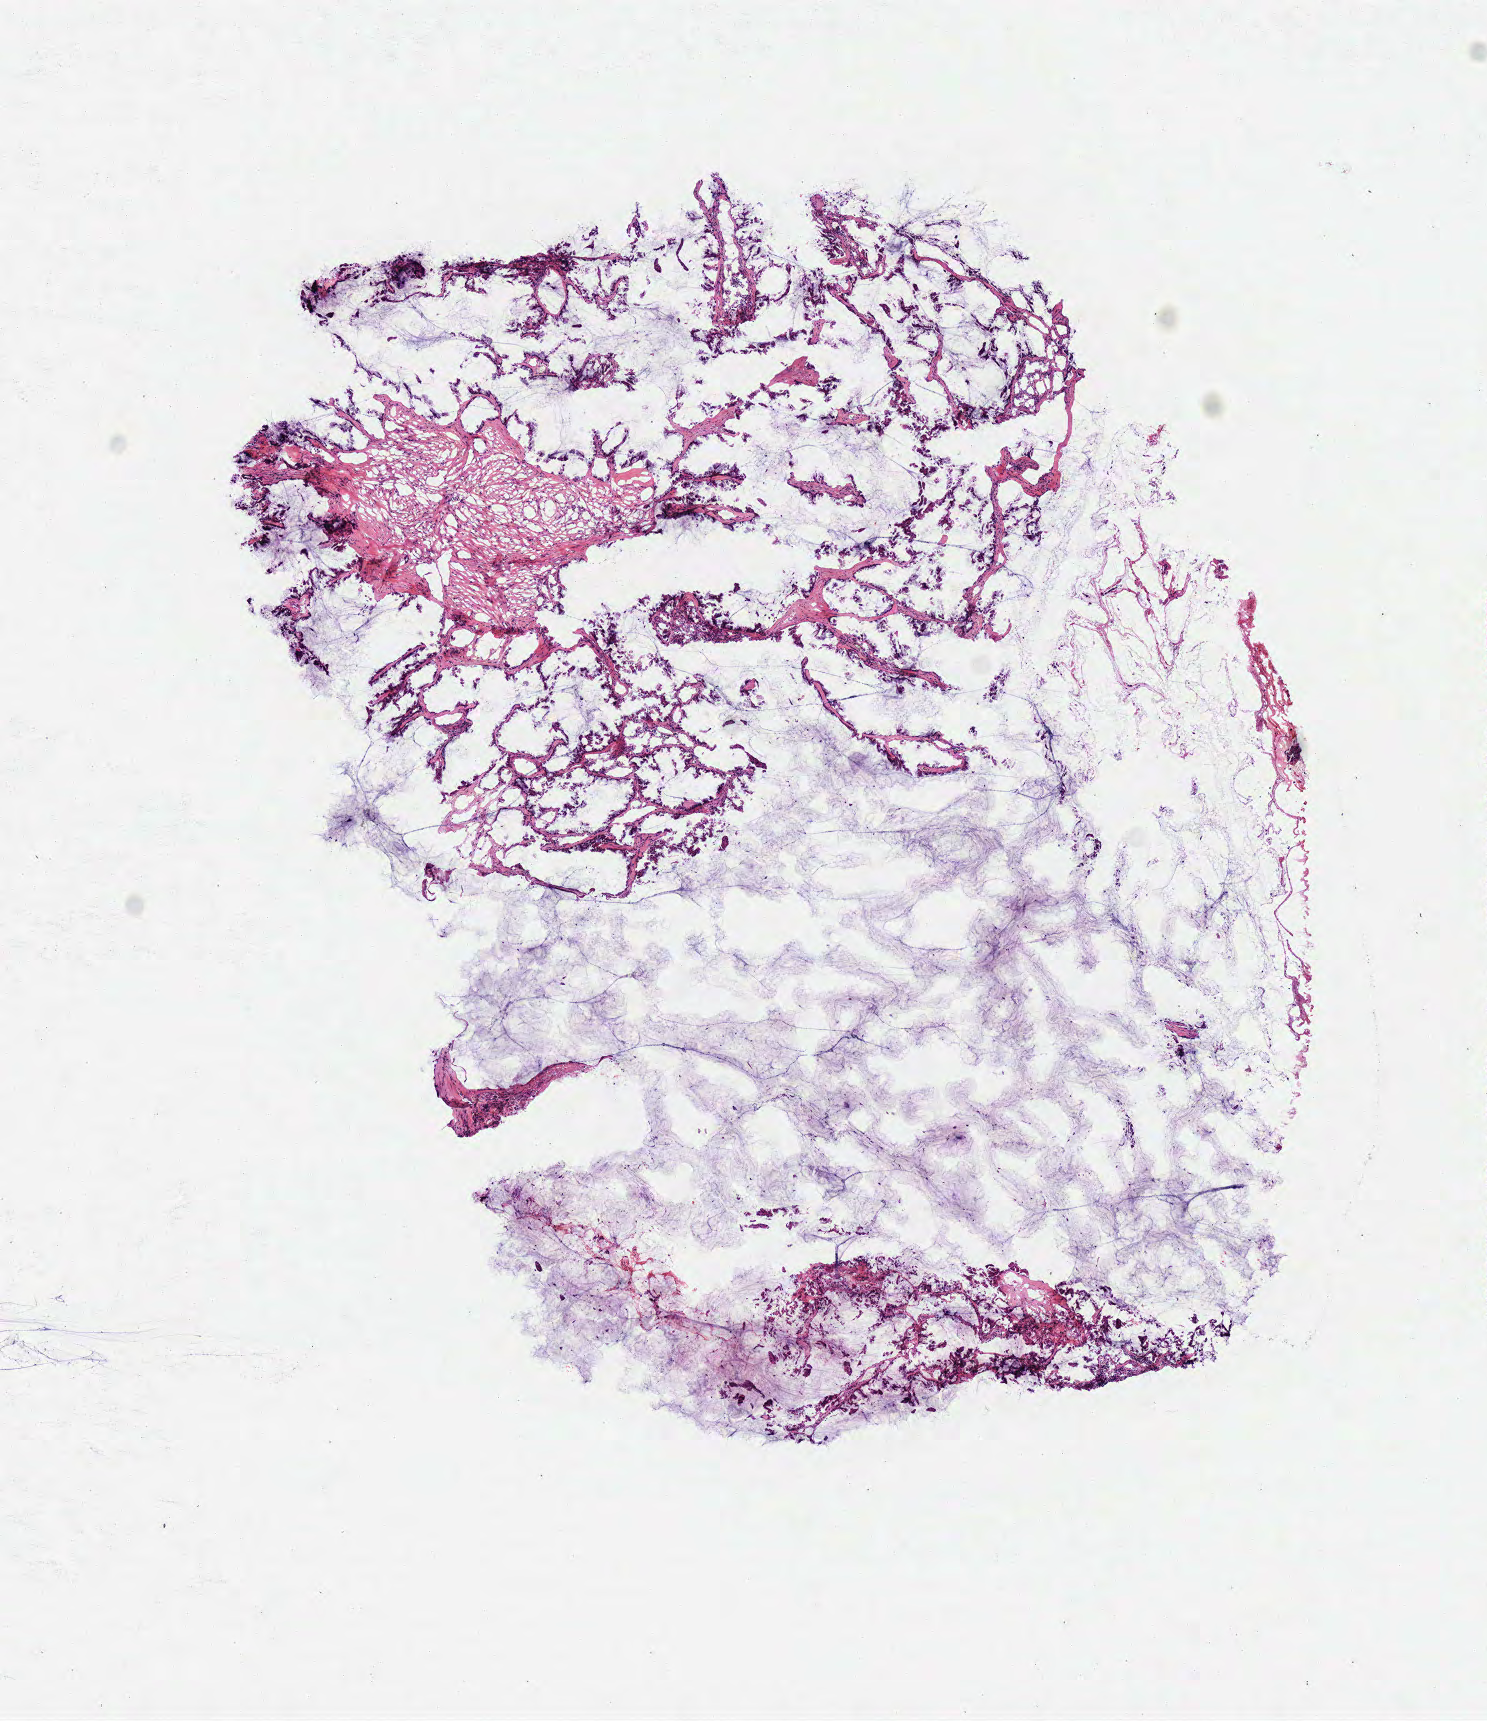
Whole-slide histology image, H&E-stained, a low-resolution overview of the entire scanned area, about 5.9 x 6.8 mm (acquisition: 40x scan). Frozen section from the top of the tissue portion. Sample: primary tumour, lung. Male, age 60 years at initial diagnosis. Composition of this section per pathologist review: tumour cells 65%, tumour nuclei 80%, normal cells 0%, stromal cells 35%, necrosis 0%.
AJCC pathologic stage: IB (6th edition). Pathologic diagnosis: Adenocarcinoma, NOS (lower lobe, lung).